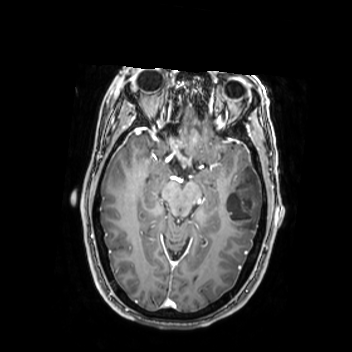
Brain MRI from a brain-tumour surgery series, one axial slice. Slice 157 of 350 in the series (ordered by position). T1-weighted post-contrast. 0.9 mm slice thickness. 352 × 352 image matrix, field of view 280 × 280 mm. From the clinical record (not read from this slice): histopathology: Oligodendroglioma; WHO grade: 2.
Outlined on this slice (manually delineated by an expert):
- tumour: box from (x=224, y=164) to (x=262, y=233) px